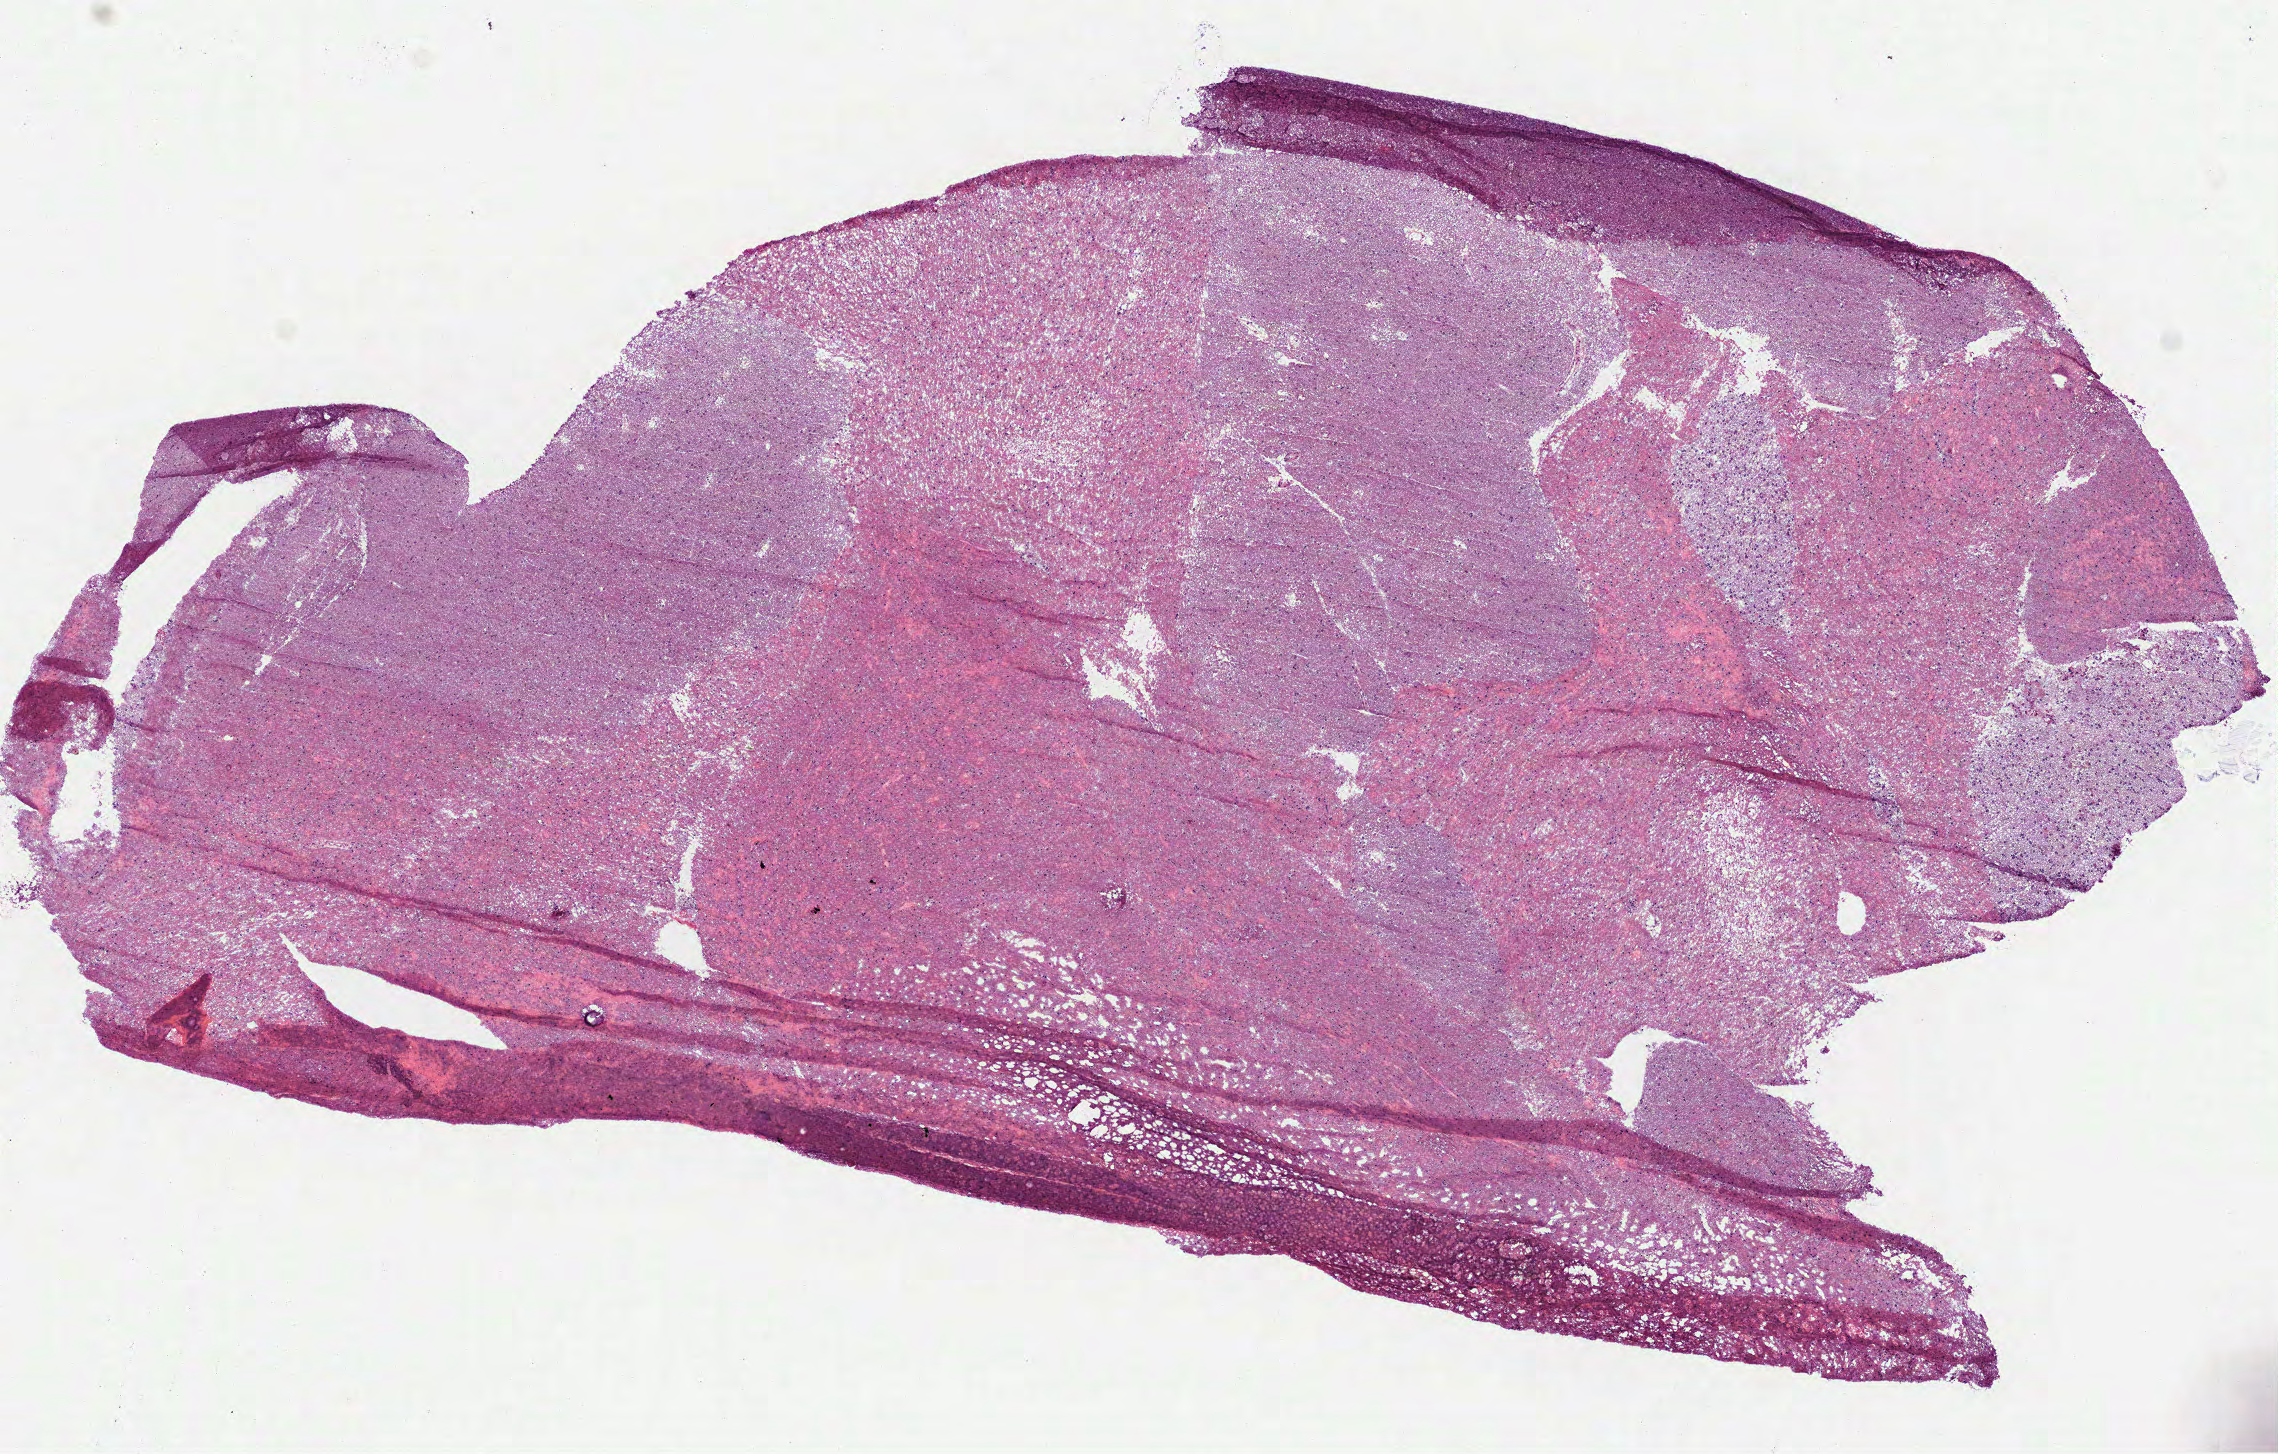
Digitized H&E tissue section (whole slide), shown as a low-resolution overview of the whole scanned area (about 9.2 x 5.9 mm, slide scanned at 40x), frozen section from the bottom of the tissue portion, sample: primary tumour, brain. Male, age 54 years at initial diagnosis. Histologic grade: G2 (moderately differentiated). Slide review estimates, as recorded: tumour cells 50%, tumour nuclei 15%, normal cells 50%, stromal cells 0%, necrosis 0%.
- diagnosis: Oligodendroglioma, NOS